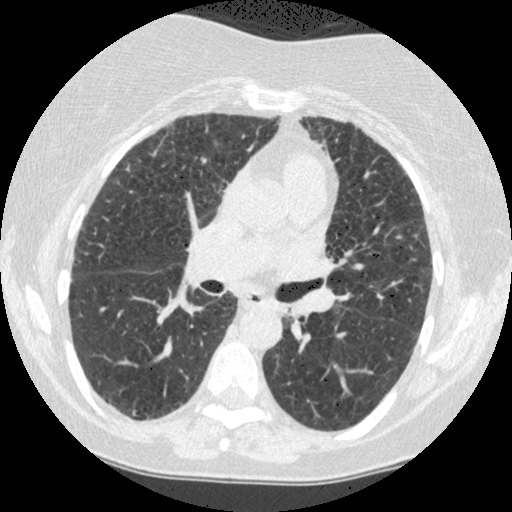
Axial slice from a low-dose chest CT screening exam. Baseline screening round. Lung window (W 1500 / L -600 HU). 1.25 mm slice thickness. Standard (soft-tissue) reconstruction kernel (STANDARD). 512 × 512 image matrix, field of view 310 × 310 mm. Female, age 60 years at enrolment. Former smoker at enrolment.
- Expert reader's lesion annotation, bounding box <273,296,312,338> (left, top, right, bottom; pixels).
- The screening reader recorded 2 non-calcified nodules or masses ≥4 mm on this exam; which of them this box marks is not recorded.
- Participant outcome: lung cancer diagnosed 794 days after this screen — small cell carcinoma, NOS, left lower lobe, undifferentiated (G4), stage IV (AJCC 6th edition), 69 mm at pathology.